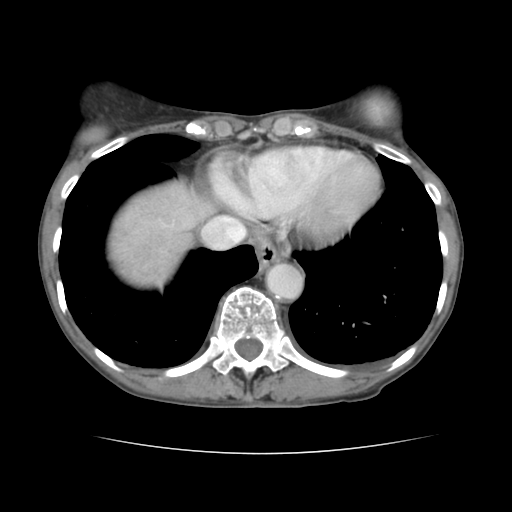
Contrast-enhanced abdominal CT, one axial slice. 120 kVp. Intravenous contrast given. Soft-tissue window (W 400 / L 40 HU). 2.5 mm slice thickness. 512 × 512 image matrix, field of view 319 × 319 mm. Female patient, age 77 years. From the clinical record (not read from this slice): diagnosis: colorectal cancer liver metastases, imaged before liver resection.
Outlined on this slice (manually delineated by an expert):
- hepatic veins: bounding box (x1, y1, x2, y2) in pixels: (202, 216, 245, 249)
- liver: (107, 184, 208, 287)